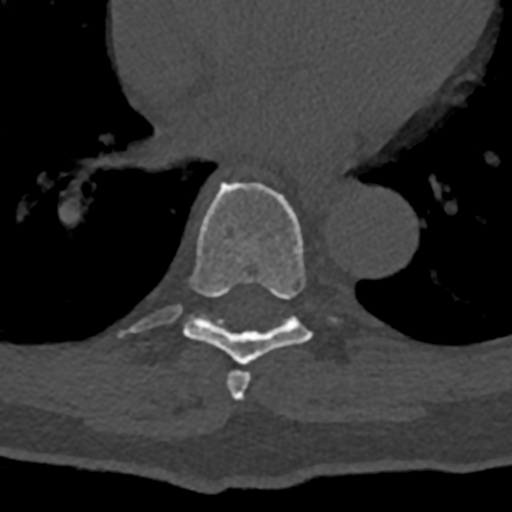
CT including the spine, one axial slice. Reconstruction kernel Br40s/3. 120 kVp. Bone window (W 1800 / L 400 HU). 0.5 mm slice thickness. 512 × 512 image matrix, field of view 160 × 160 mm. Patient: male, 74 years. Case-level facts recorded for this patient, not image findings: primary cancer: renal.
Annotated regions visible in this slice (semi-automatically segmented with operator editing):
- T7 vertebra: bounding box (x1, y1, x2, y2) in pixels: (226, 370, 251, 401)
- T8 vertebra: (119, 182, 336, 365)